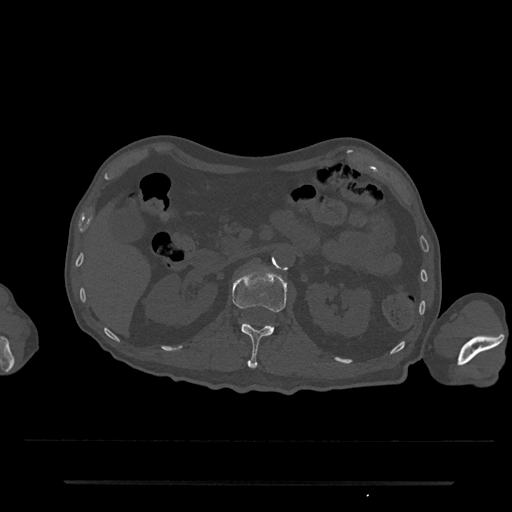
CT including the spine, one axial slice; position 117 of 797 along the scan axis; 120 kVp; bone window (W 1800 / L 400 HU); 0.5 mm slice thickness; 512 × 512 image matrix, field of view 427 × 427 mm. Male patient, age 74 years. From the clinical record (not read from this slice): primary cancer: prostate.
Outlined on this slice (semi-automatic segmentation, software-assisted and operator-edited):
- L1 vertebra: bounding box [x1, y1, x2, y2] px = [232, 268, 287, 369]